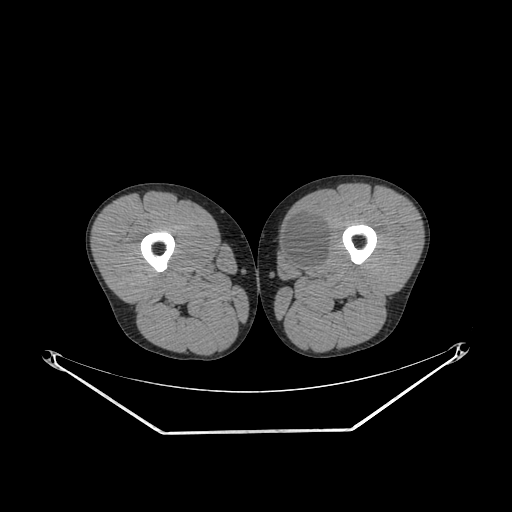
CT of an extremity soft-tissue mass (from a PET/CT study), one axial slice. Position 249 of 311 along the scan axis. Soft-tissue window (W 400 / L 40 HU). 512 × 512 image matrix. Male patient. From the clinical record (not read from this slice): histological type: mixoid liposarcoma; grade: low; site of the primary tumour: left thigh.
Annotated regions visible in this slice (expert contour drawn on MRI and transferred to this co-registered scan by the dataset authors):
- gross tumour volume (mass): box from (x=281, y=215) to (x=330, y=270) px